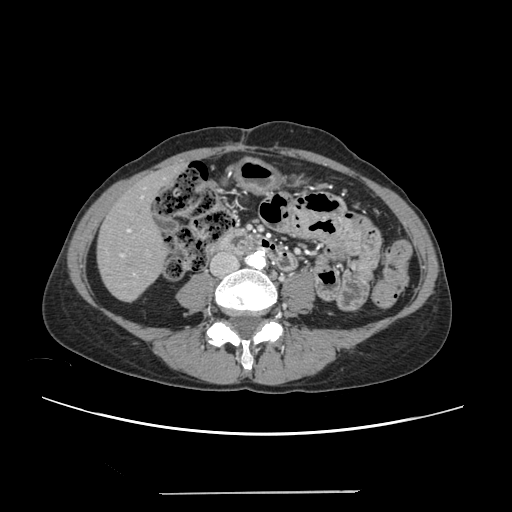
Contrast-enhanced abdominal CT, one axial slice; position 55 of 240 along the scan axis; 120 kVp; intravenous contrast given; soft-tissue window (W 400 / L 40 HU); 1.25 mm slice thickness; 512 × 512 image matrix. Female patient, age 60 years. From the clinical record (not read from this slice): diagnosis: colorectal cancer liver metastases, imaged before liver resection; multiple liver metastases: no; largest metastasis: 1.5 cm; disease in both lobes: no.
Annotated regions visible in this slice (manually delineated by an expert):
- liver: bounding box [x1, y1, x2, y2] px = [98, 168, 179, 301]
- planned liver remnant (the part of the liver to remain after resection): [98, 171, 171, 301]
- portal vein (with intrahepatic branches): [120, 187, 146, 277]